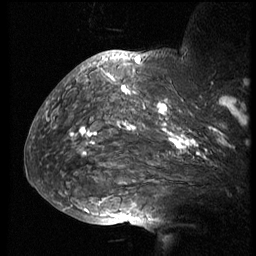
Breast MRI (dynamic contrast-enhanced), one sagittal slice. 3 images stored at this slice position (order not interpretable as contrast timing). 1.5 T. TE 4.2 ms, TR 8.9 ms. 2.5 mm slice thickness. 256 × 256 image matrix. Female patient, age 57 years. Case-level facts recorded for this patient, not image findings: setting: breast cancer imaged before/during neoadjuvant chemotherapy; receptor status: HER2-positive.
Structures marked on this image (semi-automatic segmentation, software-assisted and operator-edited):
- analysis volume of interest (the breast-tissue region the enhancement analysis was run in; not a lesion): bounding box [x1, y1, x2, y2] px = [51, 67, 249, 173]
- tumour enhancement mask (voxels above the 140 % enhancement threshold inside the analysis volume of interest): [72, 75, 247, 159]